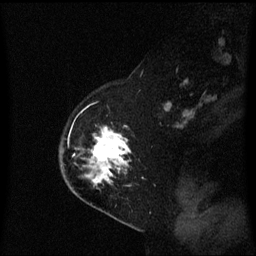
Breast MRI (dynamic contrast-enhanced), one sagittal slice. Slice 43 of 60 in the series (ordered by position). Dynamic contrast-enhanced series, image 2 of 3 at this slice position (ordered by acquisition). 1.5 T. TE 4.2 ms, TR 8.4 ms. 2 mm slice thickness. 256 × 256 image matrix, field of view 210 × 210 mm. Female patient, age 54 years. Case-level facts recorded for this patient, not image findings: setting: breast cancer imaged before/during neoadjuvant chemotherapy; receptor status: HER2-positive.
Structures marked on this image (semi-automatically segmented with operator editing):
- analysis volume of interest (the breast-tissue region the enhancement analysis was run in; not a lesion): bounding box (x1, y1, x2, y2) in pixels: (62, 129, 133, 199)
- tumour enhancement mask (voxels above the 70 % enhancement threshold inside the analysis volume of interest): (90, 130, 132, 185)